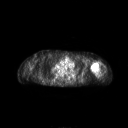
FDG PET of an extremity soft-tissue mass (from a PET/CT study), one axial slice; slice 179 of 267 in the series (ordered by position); 3.27 mm slice thickness; 128 × 128 image matrix, field of view 700 × 700 mm. Patient: female, 83 years. From the clinical record (not read from this slice): histological type: pleiomorphic leiomyosarcoma; grade: high; site of the primary tumour: left biceps.
Annotated regions visible in this slice (expert contour drawn on MRI and transferred to this co-registered scan by the dataset authors):
- gross tumour volume including surrounding oedema: bounding box [x1, y1, x2, y2] px = [91, 62, 100, 76]
- gross tumour volume (mass): [91, 62, 100, 73]